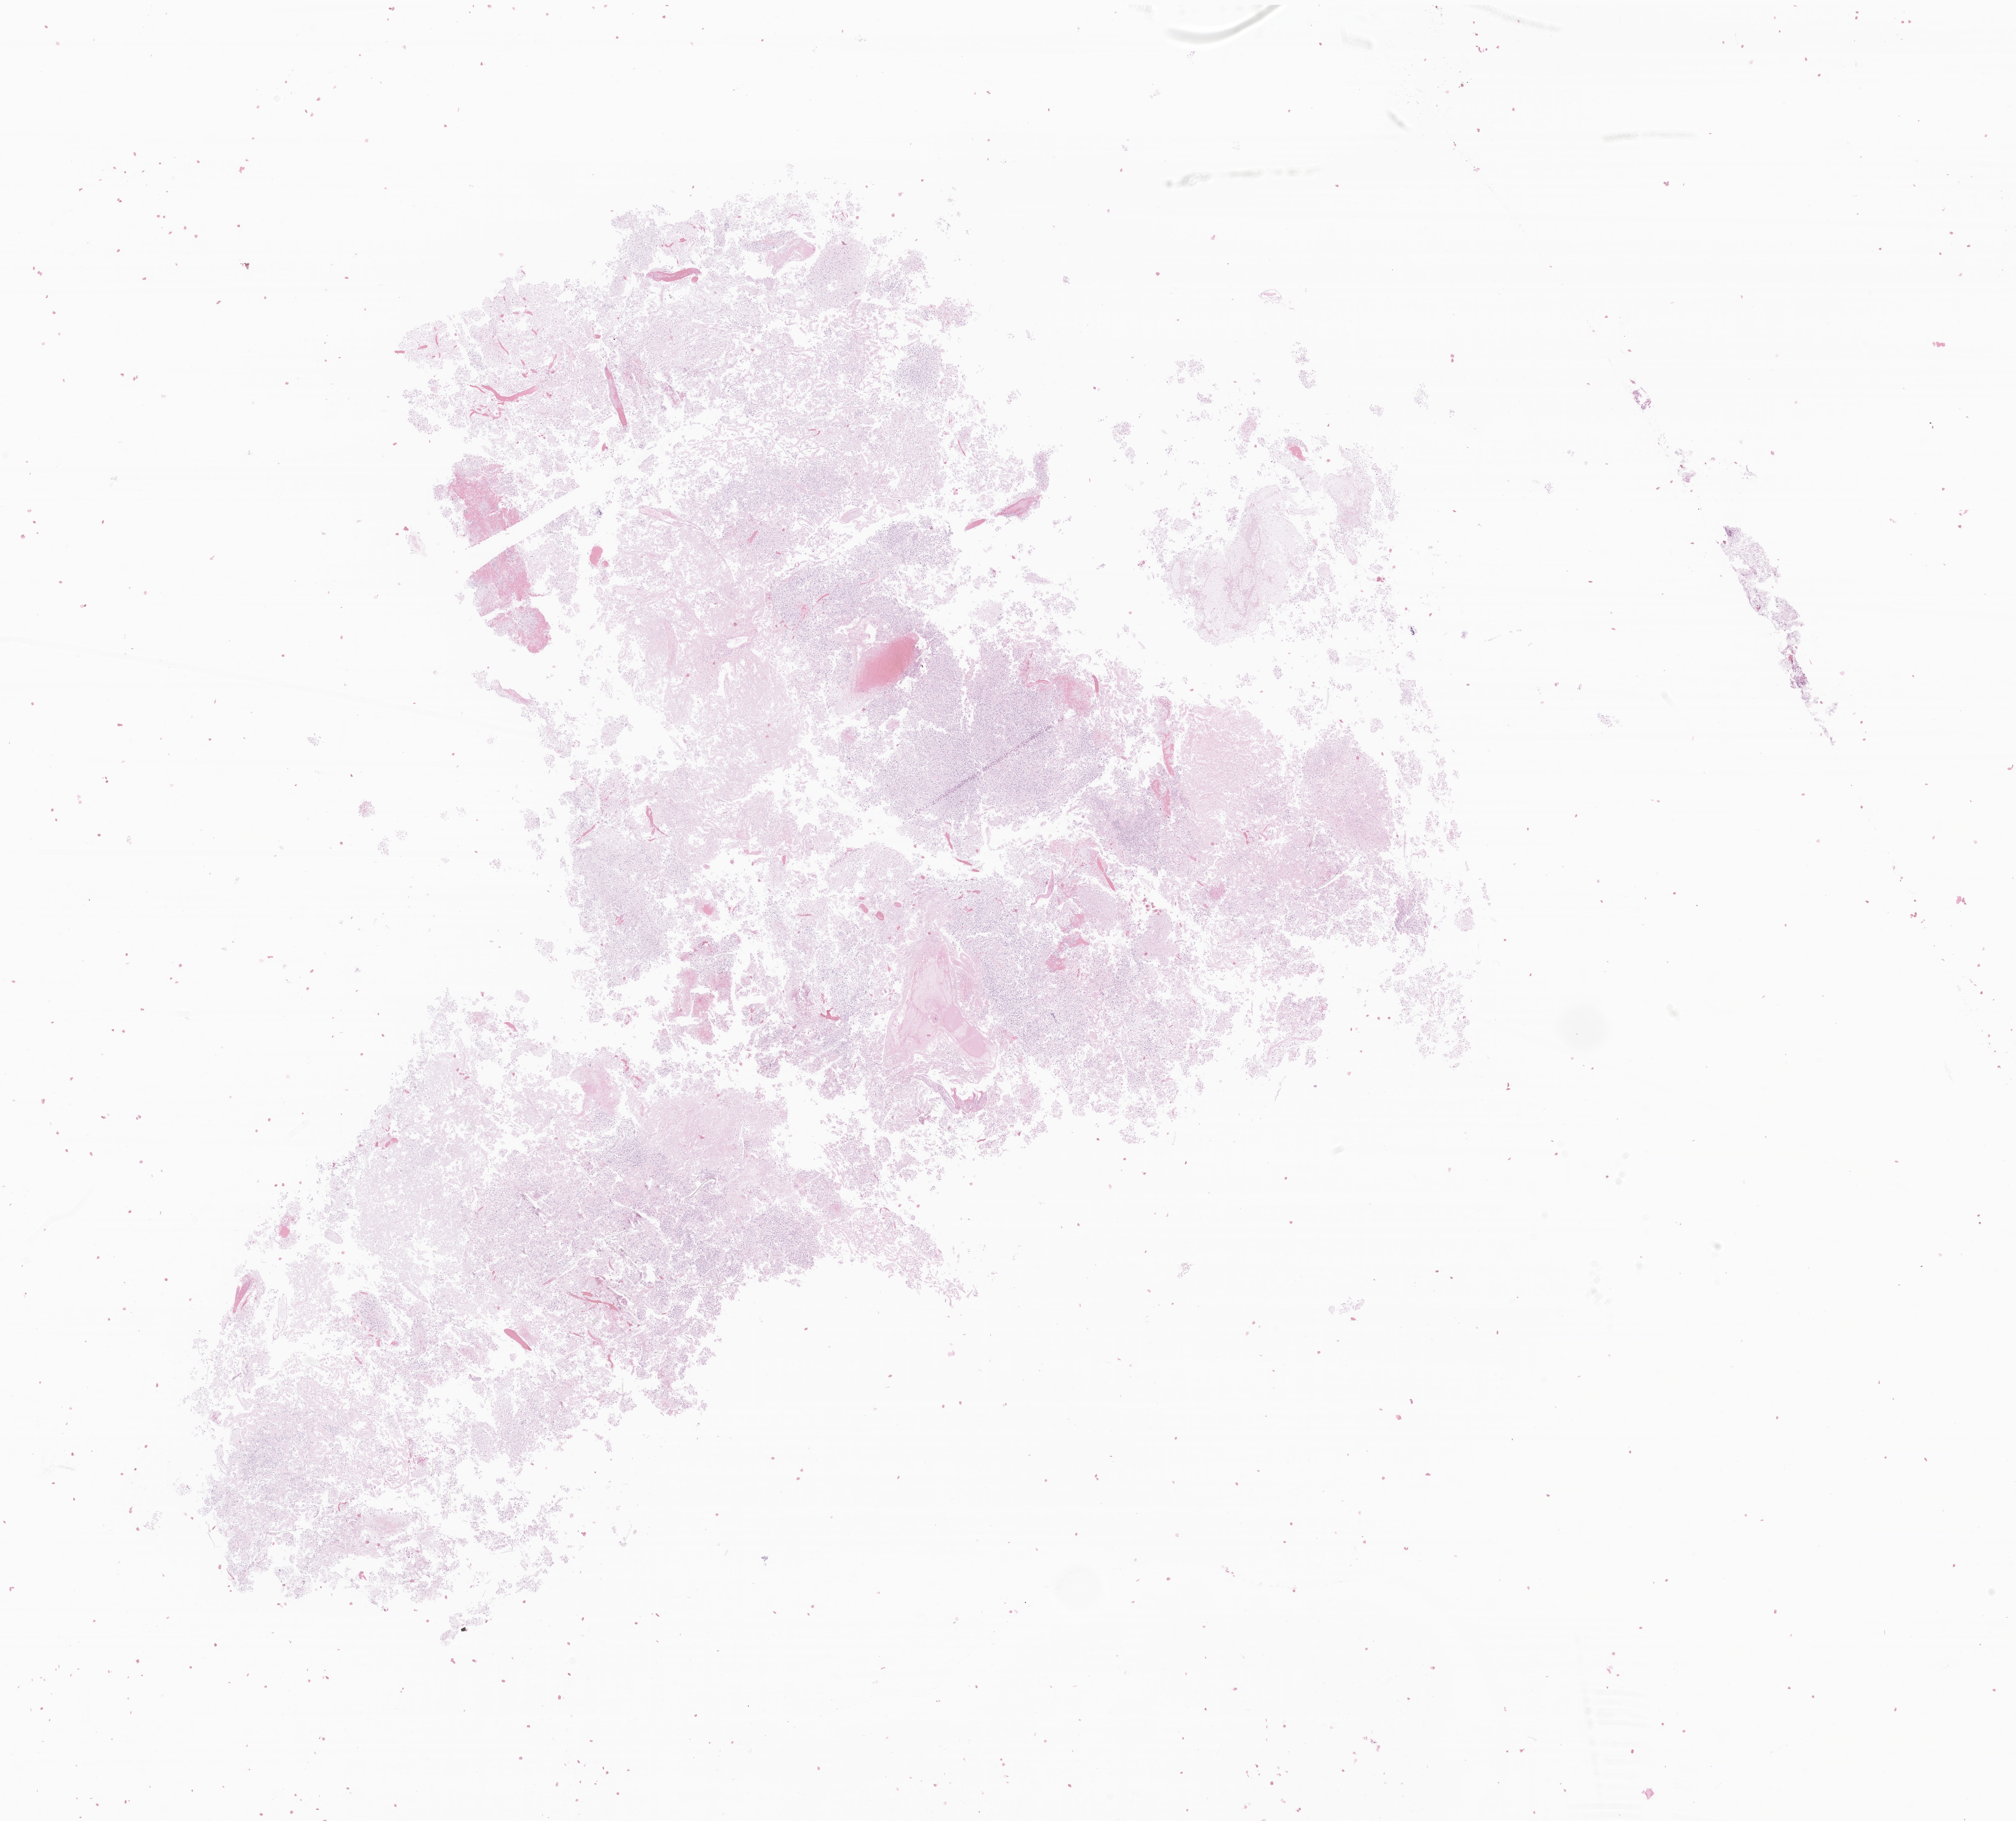
Whole-slide image, H&E stain of tumor tissue from the cerebrum, a low-resolution overview of the entire scanned area, about 20.6 x 18.6 mm. FFPE section. Female patient, age 85 months (7 years 1 month).
Diagnosis (ICD-O-3 morphology term): Glioma, malignant.